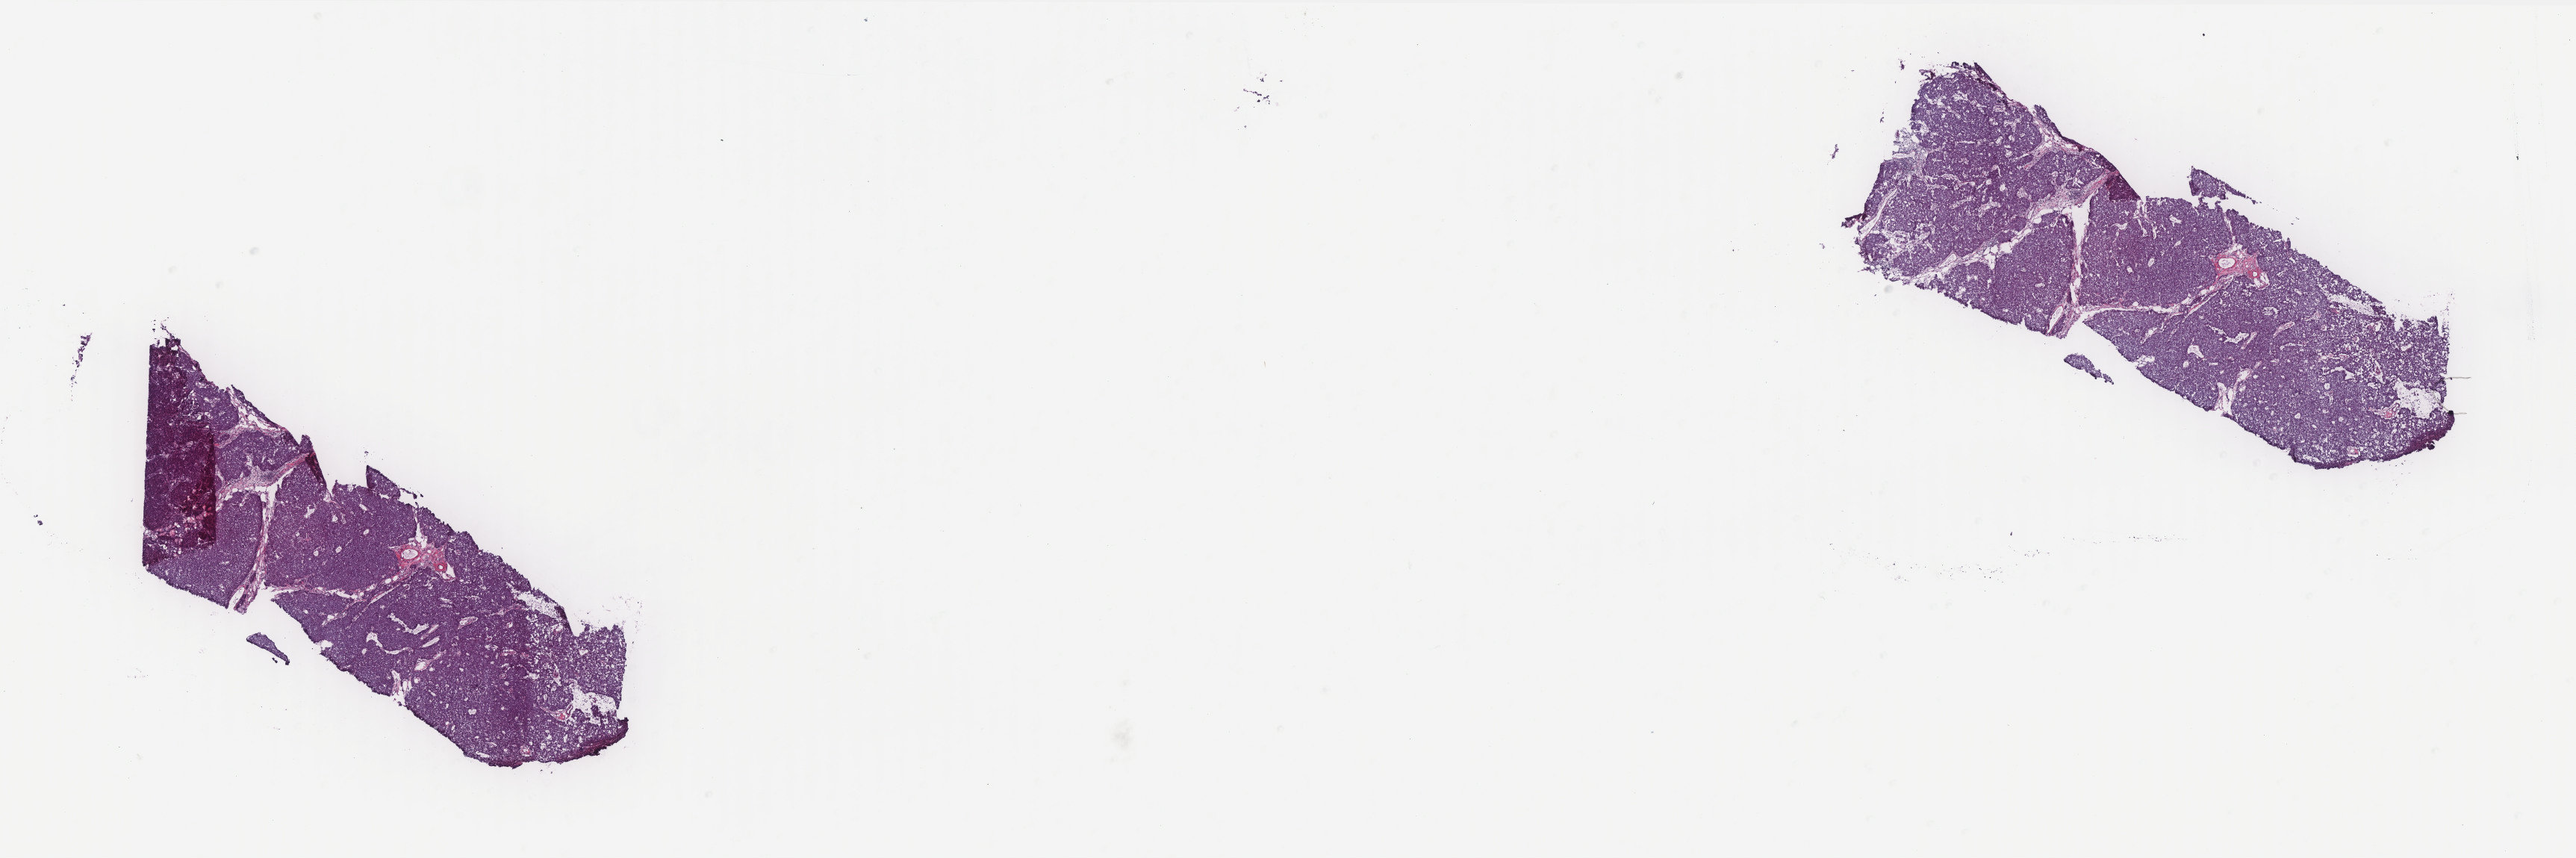
Digitized Hematoxylin and eosin (H&E) stained tissue section (whole slide), a low-resolution overview of the entire scanned area, about 27.7 x 9.2 mm (acquisition: 40x scan). Frozen section from the top of the tissue portion. Sample: primary tumour, breast. Female, age 63 years at initial diagnosis. Slide review estimates, as recorded: tumour cells 100%, tumour nuclei 95%, normal cells 0%, stromal cells 0%, necrosis 0%. Infiltration values recorded for this section: lymphocyte infiltration 0%, monocyte infiltration 0%, neutrophil infiltration 0%.
Laterality: right. Lymph nodes positive (case pathology): 0 of 2 examined. Histologic diagnosis: Infiltrating duct carcinoma, NOS. AJCC pathologic stage: IIA (6th edition).